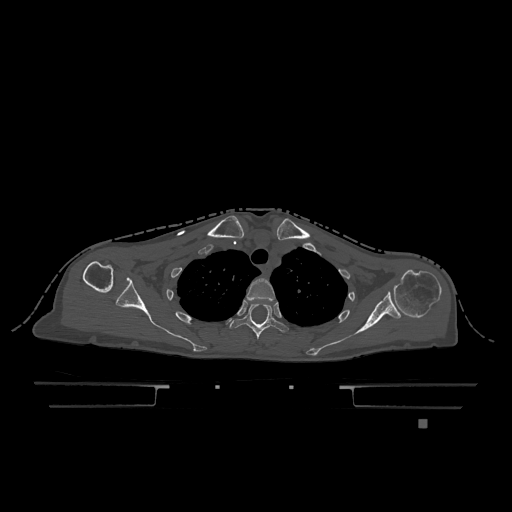
CT including the spine, one axial slice; bone window (W 1800 / L 400 HU); 512 × 512 image matrix. Female patient, age 74 years. From the clinical record (not read from this slice): primary cancer: lung; vertebrae with lytic lesions (as recorded): T1, T4, T5, T6, L4, L5.
Structures marked on this image (semi-automatically segmented with operator editing):
- T2 vertebra: bounding box <246,278,275,301> (left, top, right, bottom; pixels)
- T3 vertebra: <230,304,289,339>